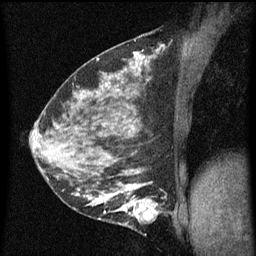
Breast MRI (dynamic contrast-enhanced), one sagittal slice. Slice 29 of 60 in the series (ordered by position). Dynamic contrast-enhanced series, image 2 of 5 at this slice position (ordered by acquisition). 1.5 T. TE 4.2 ms, TR 8 ms. 2 mm slice thickness. 256 × 256 image matrix, field of view 180 × 180 mm. Female patient, age 35 years.
Annotated regions visible in this slice (semi-automatic segmentation, software-assisted and operator-edited):
- analysis volume of interest (the breast-tissue region the enhancement analysis was run in; not a lesion): bounding box (x1, y1, x2, y2) in pixels: (118, 190, 165, 229)
- tumour enhancement mask (voxels above the 70 % enhancement threshold inside the analysis volume of interest): (118, 190, 159, 219)